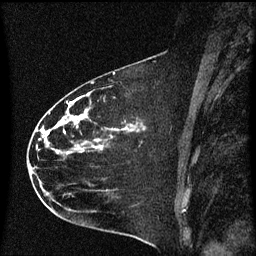
Breast MRI (dynamic contrast-enhanced), one sagittal slice. Slice 37 of 60 in the series (ordered by position). Dynamic contrast-enhanced series, image 2 of 3 at this slice position (ordered by acquisition). 1.5 T. TE 4.2 ms, TR 8.4 ms. 256 × 256 image matrix, field of view 200 × 200 mm. Patient: female, 35 years. Case-level facts recorded for this patient, not image findings: setting: breast cancer imaged before/during neoadjuvant chemotherapy; receptor status: HER2-positive.
Annotated regions visible in this slice (semi-automatic segmentation, software-assisted and operator-edited):
- analysis volume of interest (the breast-tissue region the enhancement analysis was run in; not a lesion): bounding box [x1, y1, x2, y2] px = [29, 68, 173, 173]
- tumour enhancement mask (voxels above the 70 % enhancement threshold inside the analysis volume of interest): [43, 94, 145, 155]